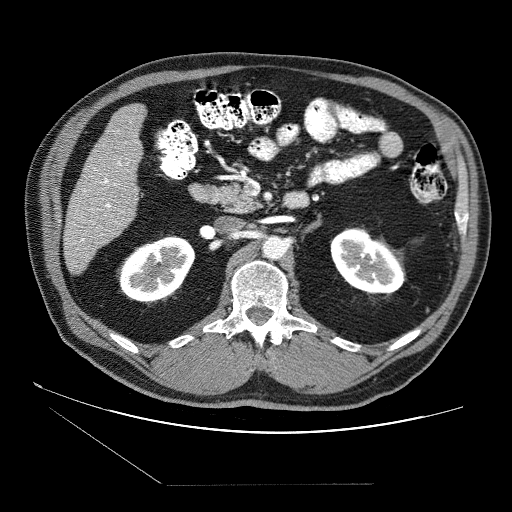
Contrast-enhanced abdominal CT (liver protocol), one axial slice; position 22 of 87 along the scan axis; reconstruction kernel STANDARD; soft-tissue window (W 400 / L 40 HU); 512 × 512 image matrix, field of view 400 × 400 mm. From the clinical record (not read from this slice): diagnosis: hepatocellular carcinoma (patient treated with transarterial chemoembolisation; whether this scan precedes or follows treatment is not stated here); TNM stage (as recorded): Stage-II; Child-Pugh class: B; tumour nodularity: multinodular; tumour size: 2.6 cm.
Outlined on this slice (semi-automatic segmentation, software-assisted and operator-edited):
- liver parenchyma outside the tumour (the mass and vessels are separate outlines, so this box may not span the whole liver): bounding box <64,104,144,274> (left, top, right, bottom; pixels)
- liver vessels: <67,142,128,266>